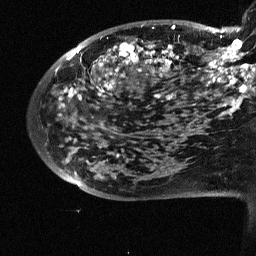
Breast MRI (dynamic contrast-enhanced), one sagittal slice. Dynamic contrast-enhanced study with each time point stored as its own series, time point 2 of 3 at this slice position (early post-contrast, ordered by acquisition time). 1.5 T. TE 4.5 ms, TR 11 ms. 2.5 mm slice thickness. 256 × 256 image matrix, field of view 200 × 200 mm. Patient: female, 38 years. Case-level facts recorded for this patient, not image findings: setting: breast cancer imaged before/during neoadjuvant chemotherapy; receptor status: HR-positive, HER2-negative.
Annotated regions visible in this slice (semi-automatic segmentation, software-assisted and operator-edited):
- analysis volume of interest (the breast-tissue region the enhancement analysis was run in; not a lesion): bounding box [x1, y1, x2, y2] px = [88, 18, 252, 126]
- tumour enhancement mask (voxels above the 90 % enhancement threshold inside the analysis volume of interest): [98, 25, 252, 112]